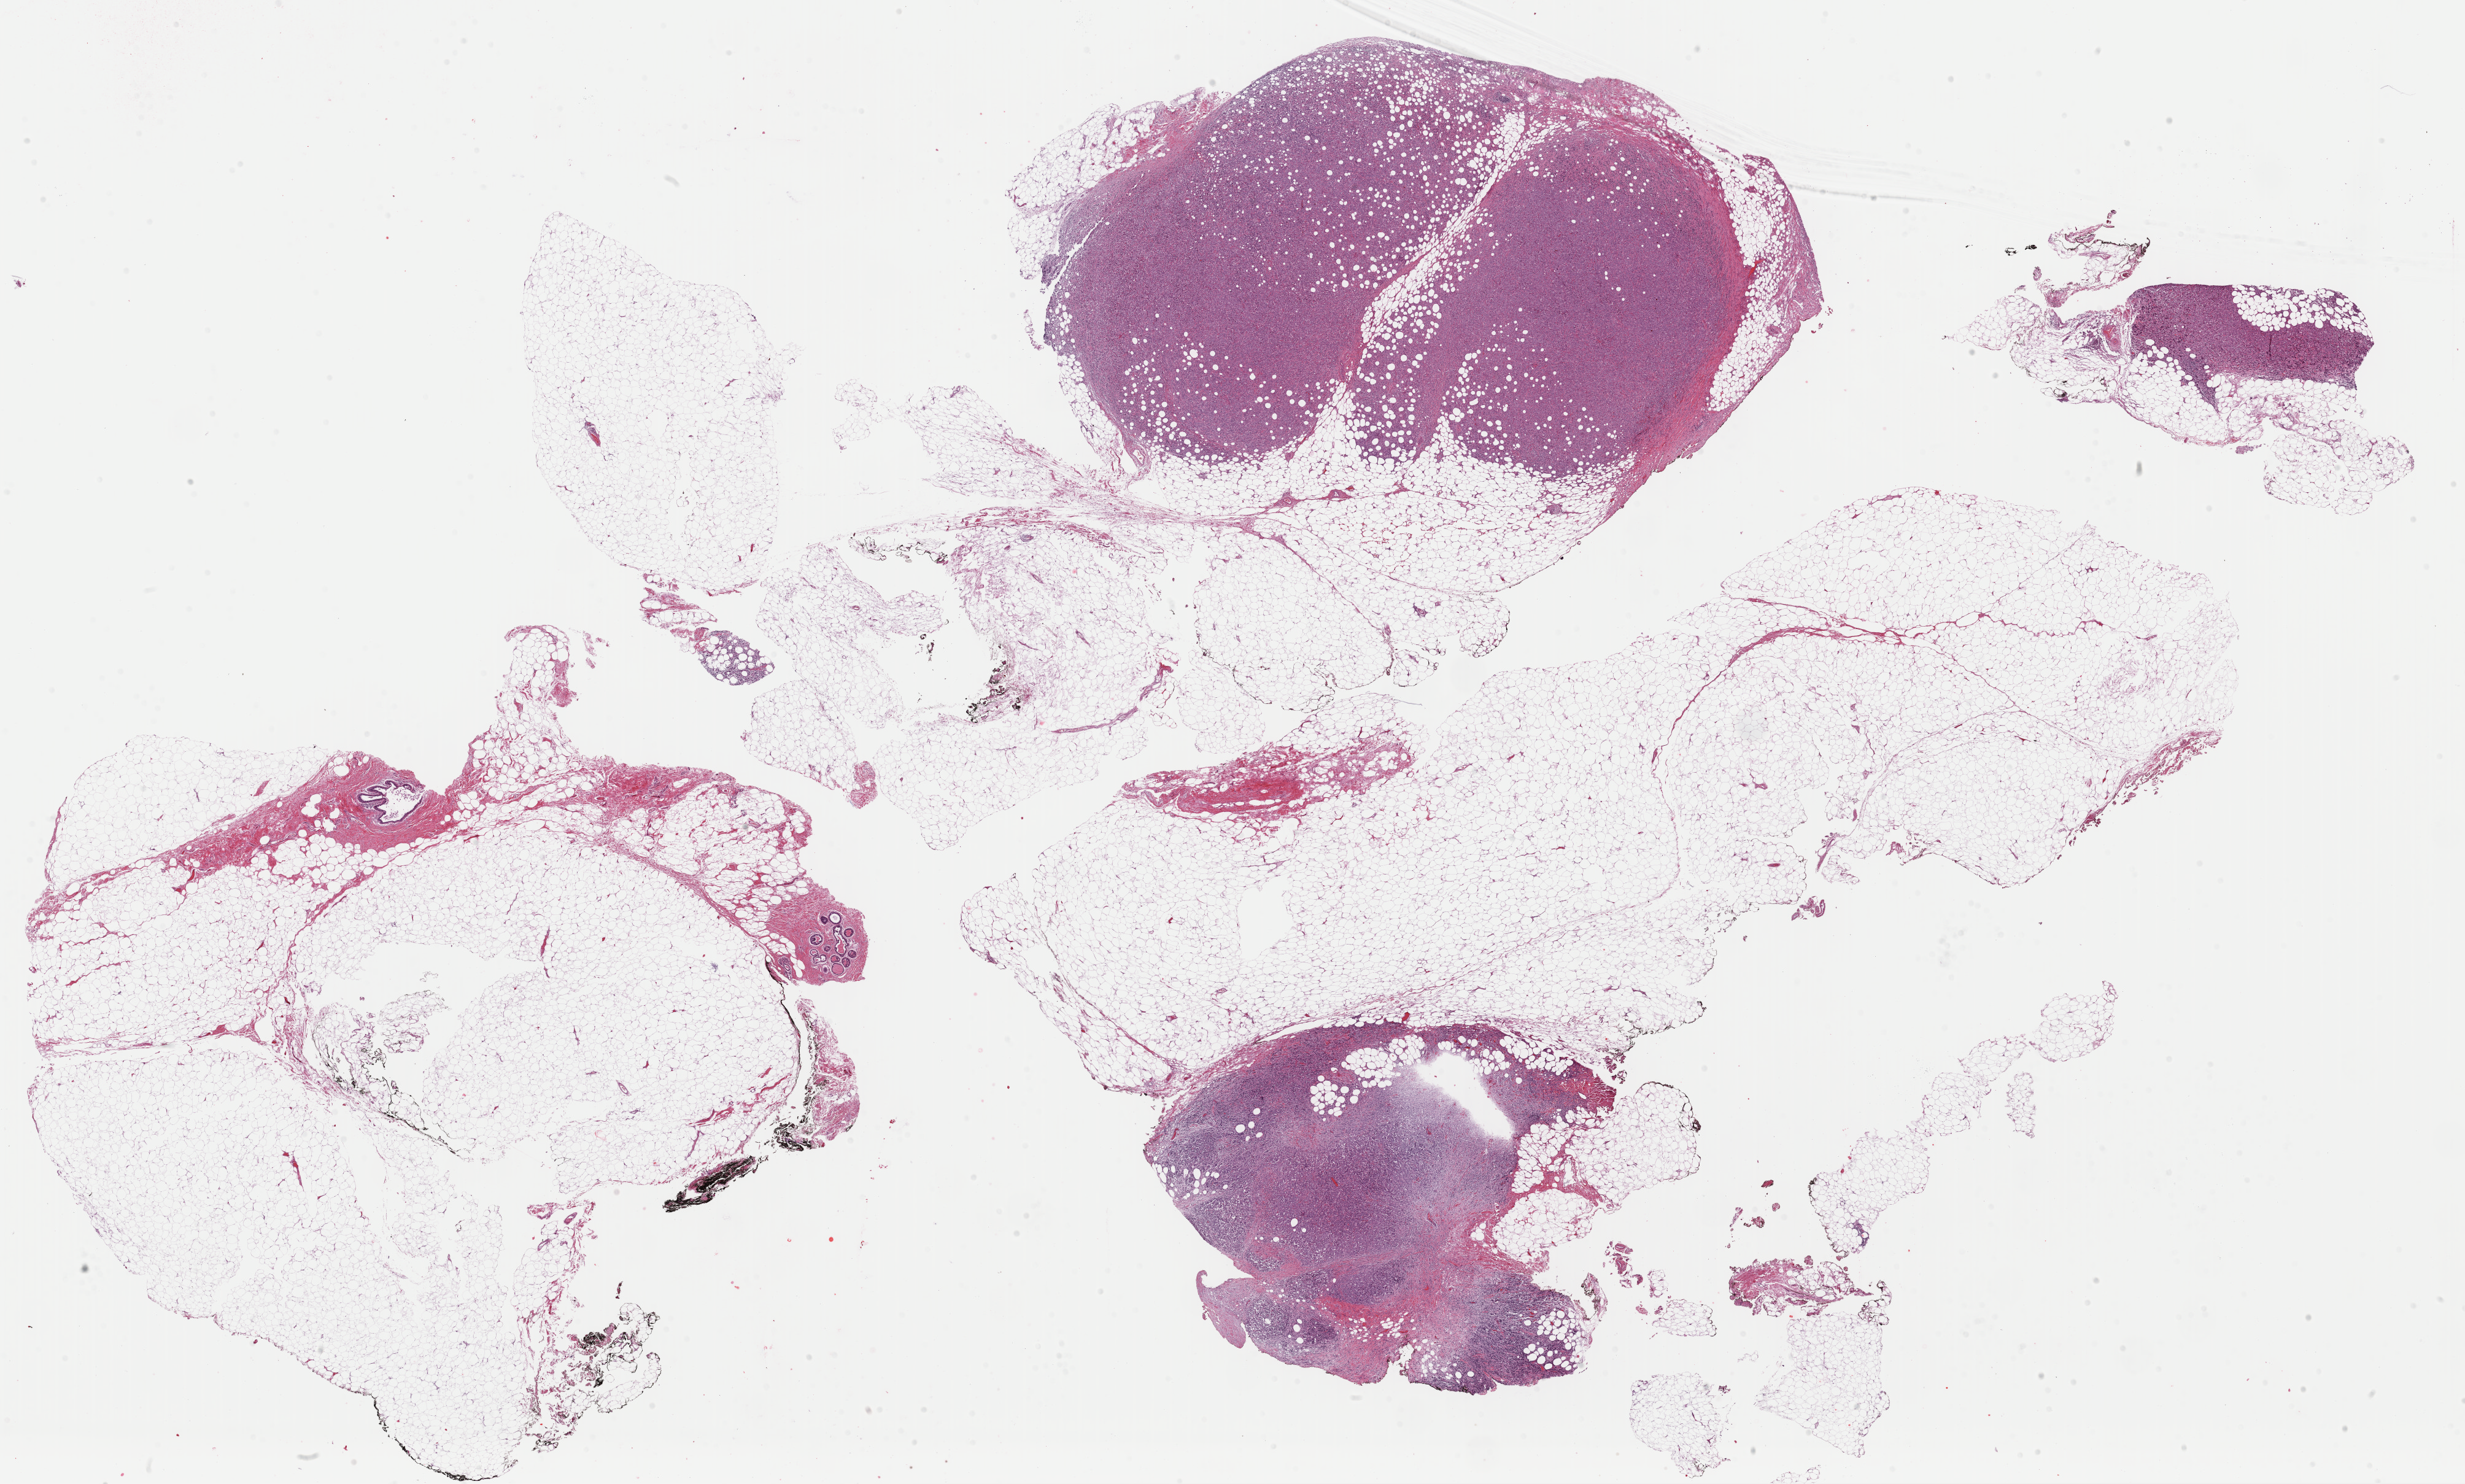
H&E-stained whole-slide image — a low-resolution overview of the entire scanned area, about 31.7 x 19.1 mm. Formalin-fixed paraffin-embedded (FFPE) diagnostic section. Breast, primary tumour sample. Patient: female, age at initial diagnosis 65 years.
* AJCC pathologic stage: IIA (5th edition)
* laterality: right
* diagnosis: Lobular carcinoma, NOS
* lymph nodes positive (case pathology): 0 of 4 examined